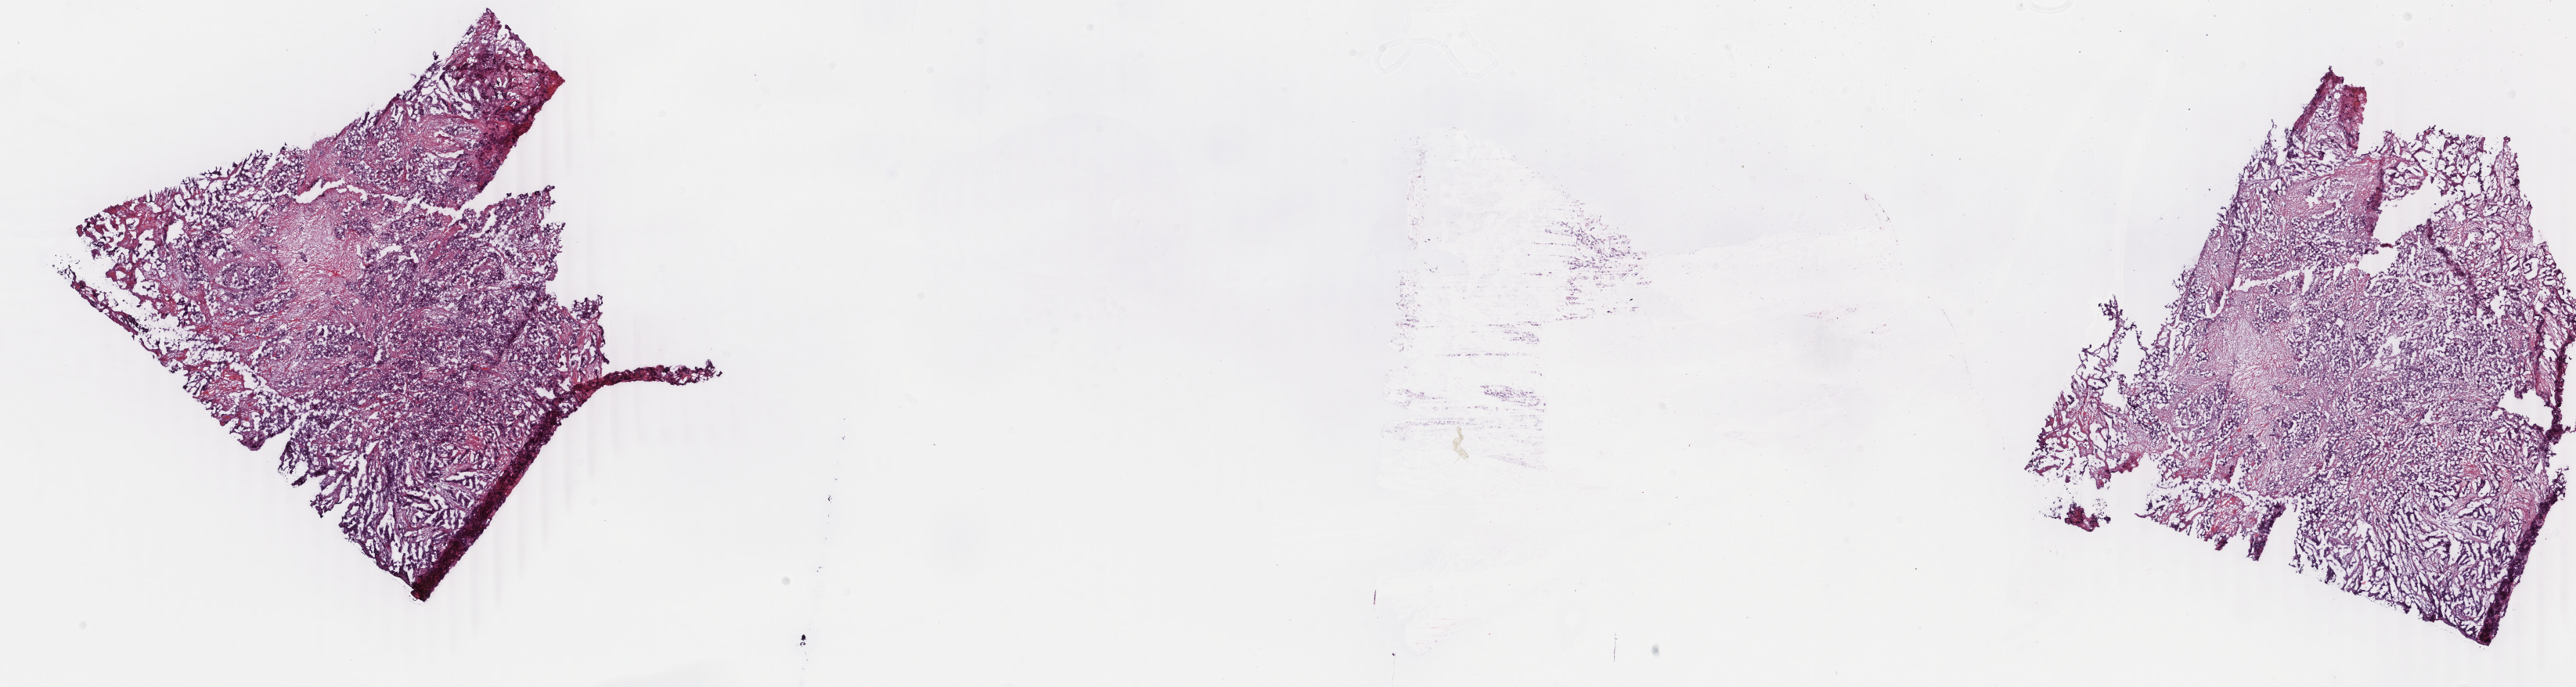
Whole-slide histology image, H&E — low-resolution overview of the scanned area, about 26.2 x 7.0 mm (from a 40x scan); frozen section from the top of the tissue portion; primary tumour sample from the breast. Patient: female, age at initial diagnosis 47 years. Slide review estimates, as recorded: tumour cells 65%, tumour nuclei 65%, normal cells 2%, stromal cells 32%, necrosis 1%. Infiltration values recorded for this section: lymphocyte infiltration 1%, monocyte infiltration 0%, neutrophil infiltration 0%.
• pathologic diagnosis: Infiltrating duct carcinoma, NOS
• AJCC pathologic stage: IIA (6th edition)
• lymph nodes positive (case pathology): 0 of 3 examined